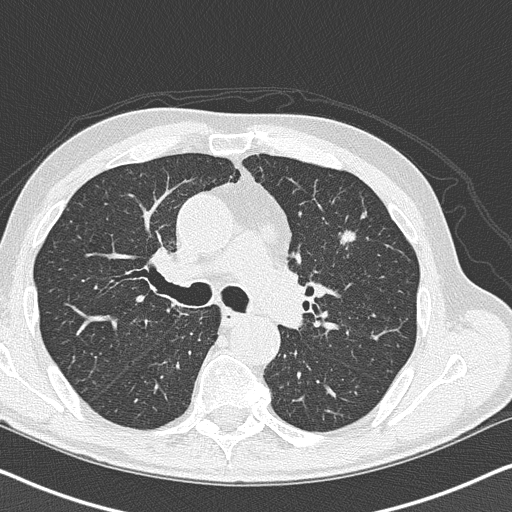
Low-dose screening chest CT, axial slice; second screening round (one year after baseline); lung window (W 1500 / L -600 HU); 2 mm slice thickness. Male, age 73 years at enrolment. Current smoker at enrolment.
• Lesion marked by an expert reader, box from (x=315, y=218) to (x=376, y=269) px.
• The screening reader recorded 3 non-calcified nodules or masses ≥4 mm on this exam (left upper lobe, left upper lobe, right lower lobe); which of them this box marks is not recorded.
• Participant outcome: lung cancer diagnosed 36 days after this screen — small cell carcinoma, NOS, left upper lobe, stage IIIB (AJCC 6th edition), 19 mm at pathology.